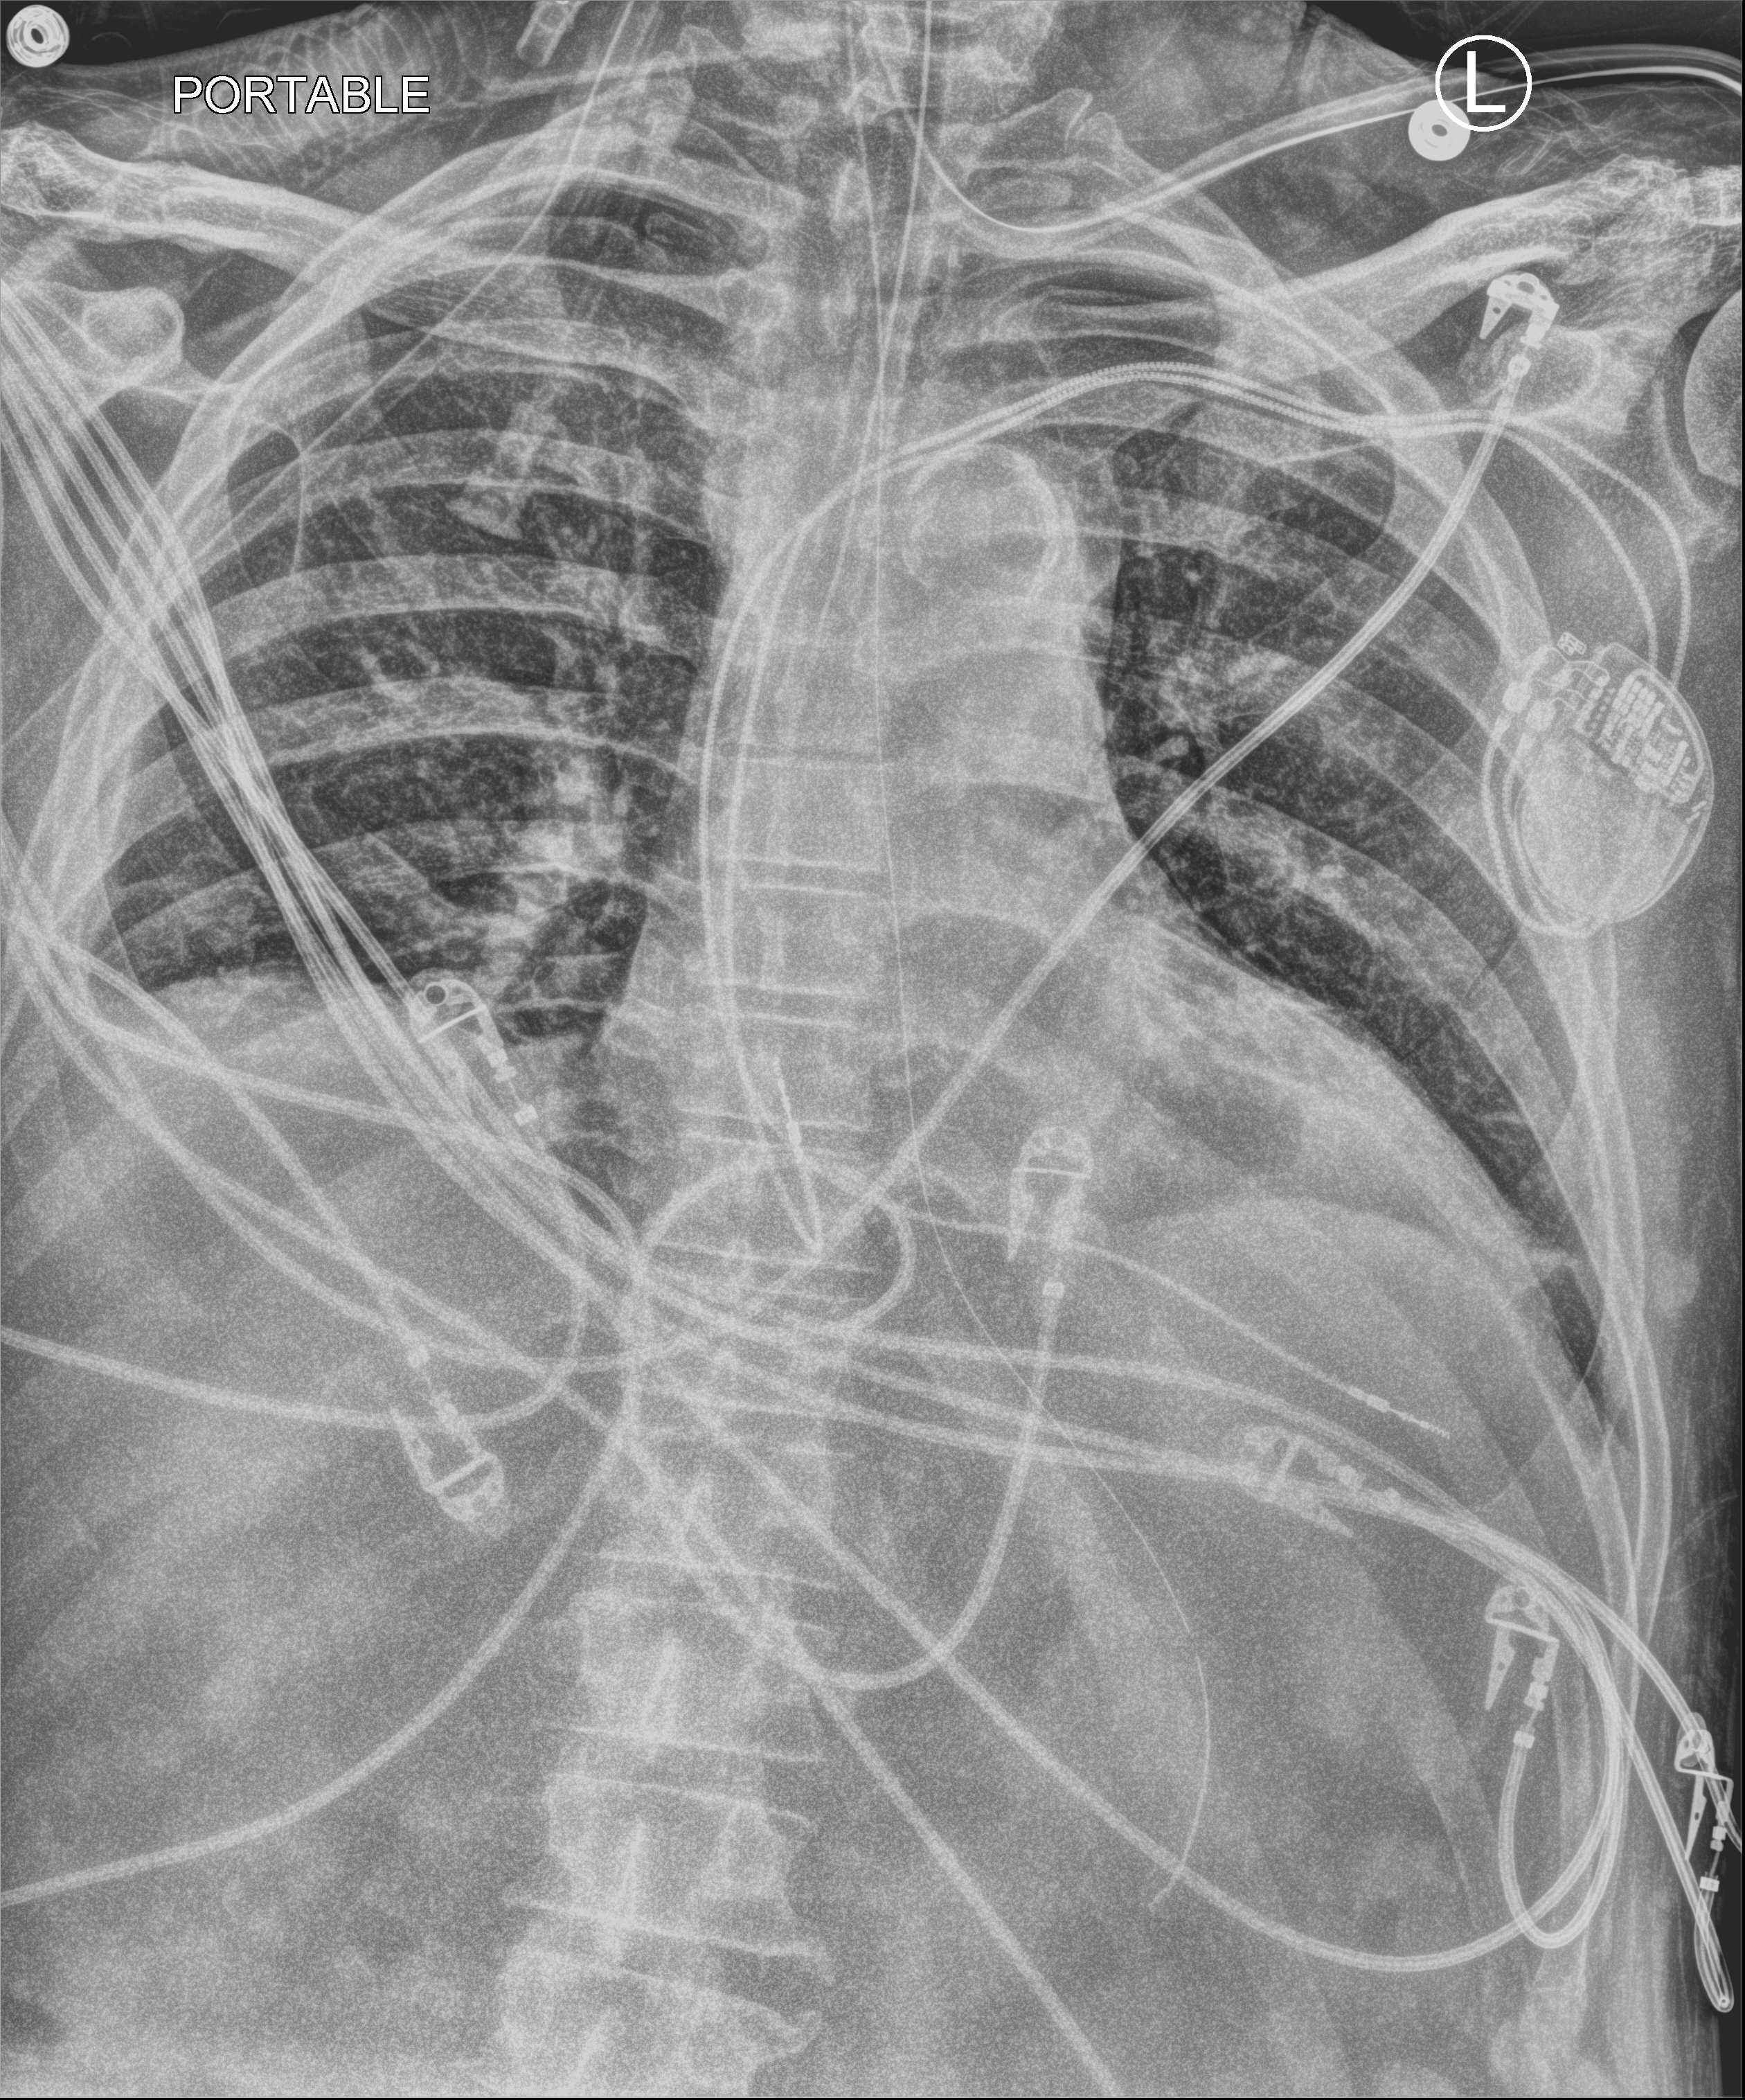
Portable chest radiograph. Male patient hospitalised with COVID-19, age 60–74 years.
Hospital-stay facts (about this admission, not read from this image; timing relative to this image not recorded): admitted to intensive care during this hospital stay: yes.